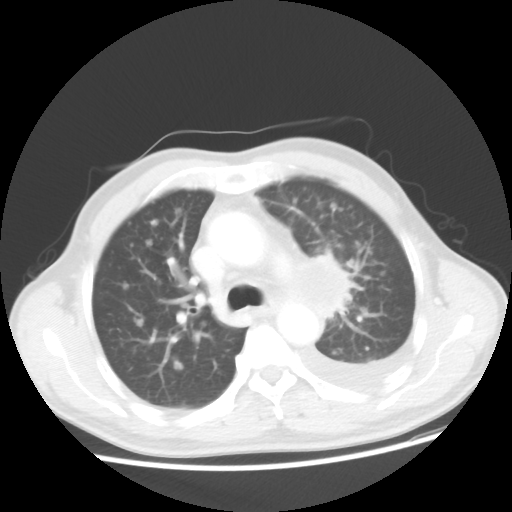
Chest CT, one axial slice; slice 32 of 48 in the series (ordered by position); reconstruction kernel STANDARD; 100 kVp; lung window (W 1500 / L -600 HU); 512 × 512 image matrix, field of view 362 × 362 mm. Male patient, age 55 years. From the clinical record (not read from this slice): clinical TNM (as recorded): T2 N3 M1a.
Structures marked on this image (bounding box drawn by a radiologist):
- lung tumour (recorded histology: squamous cell carcinoma): bounding box <295,251,356,339> (left, top, right, bottom; pixels)